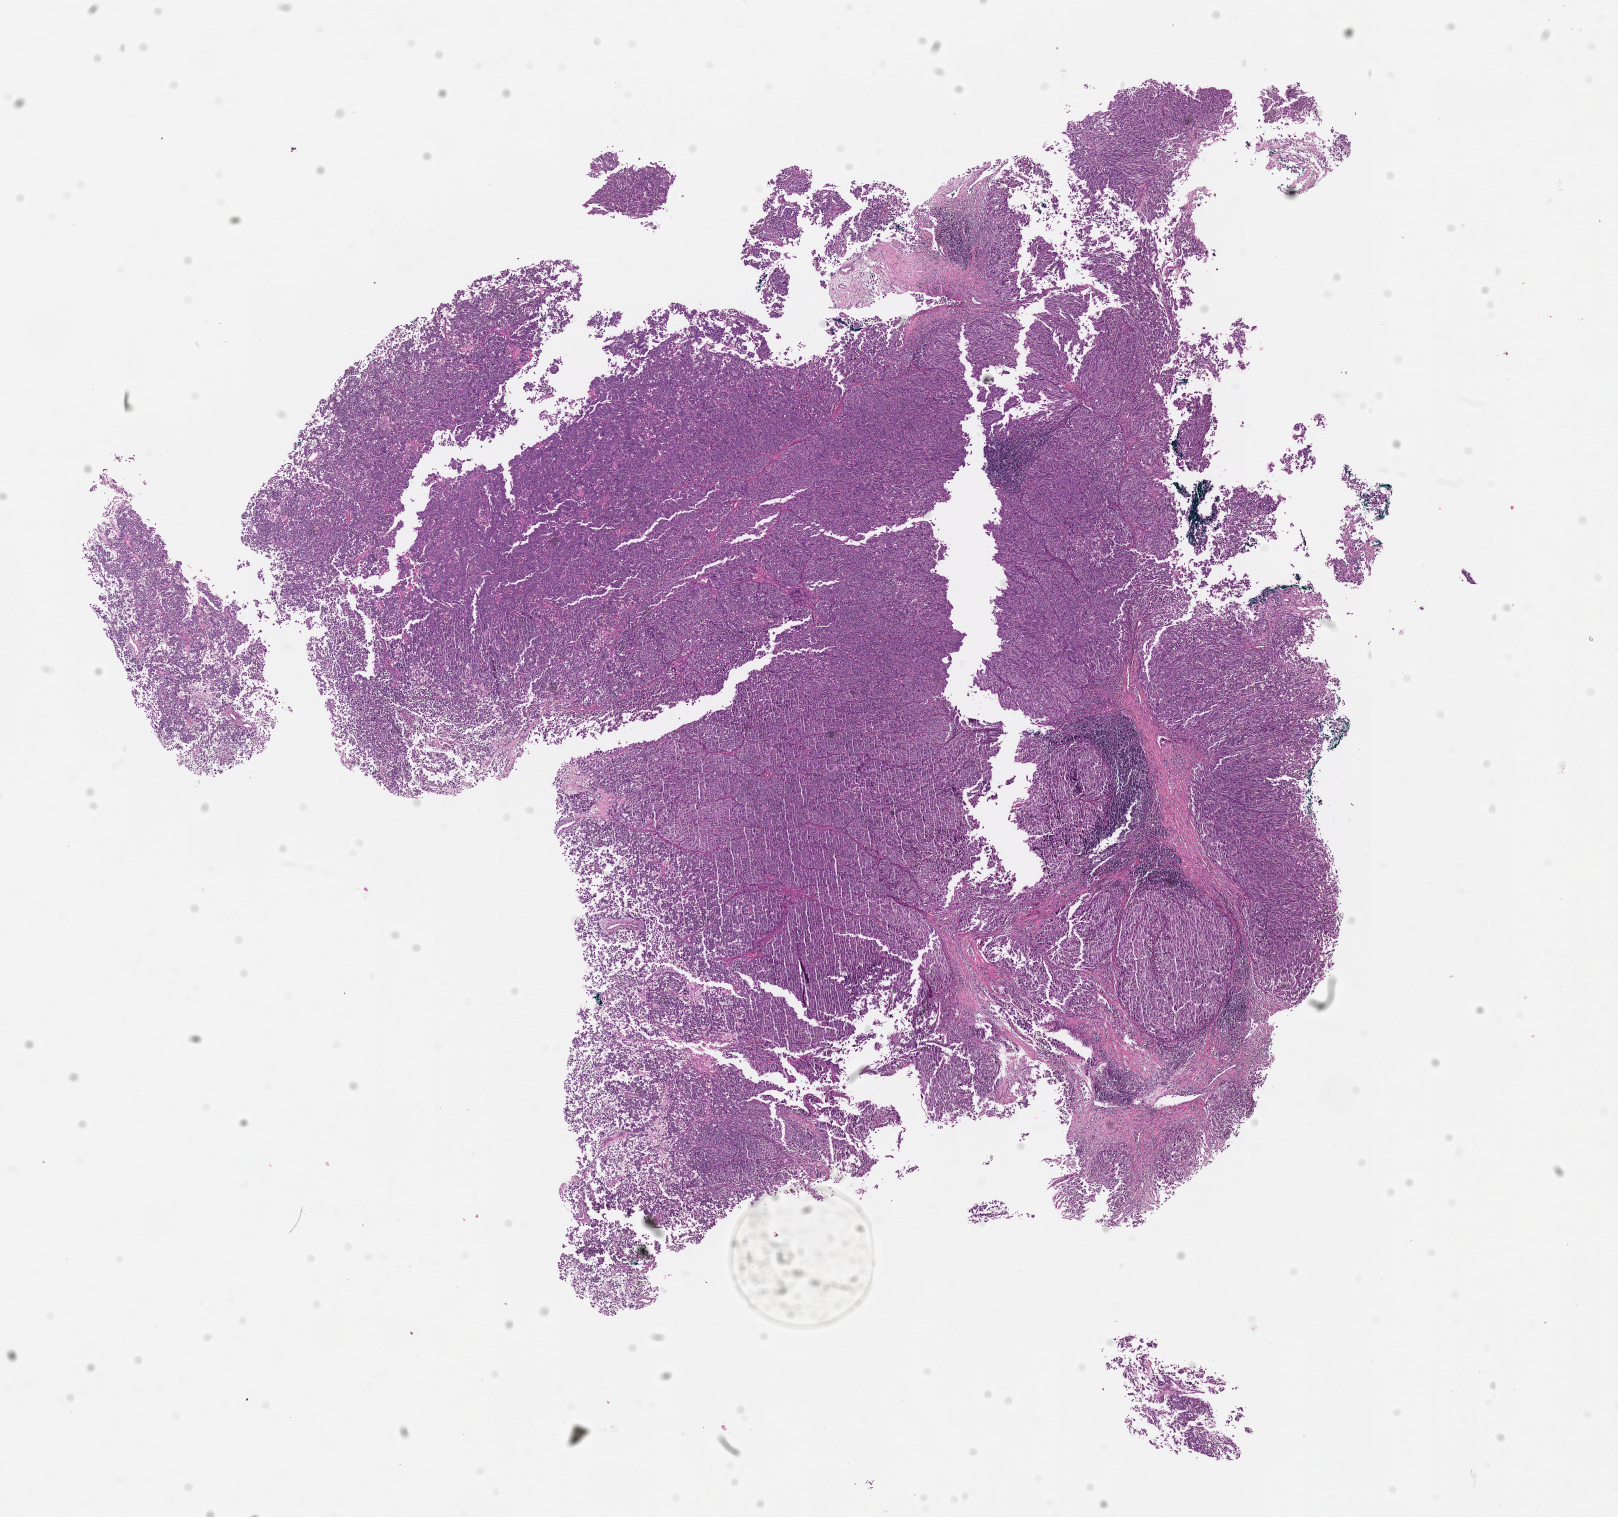
Whole-slide histology image, H&E — low-resolution overview of the scanned area, about 13.0 x 12.2 mm (acquisition: 20x scan); tumour tissue sample, sampled site: lymph node. 41-year-old male patient. Composition of this section per pathologist review: tumour nuclei 80%, necrosis 0%.
• this section: metastatic tumour tissue
• patient diagnosis: Malignant melanoma, NOS